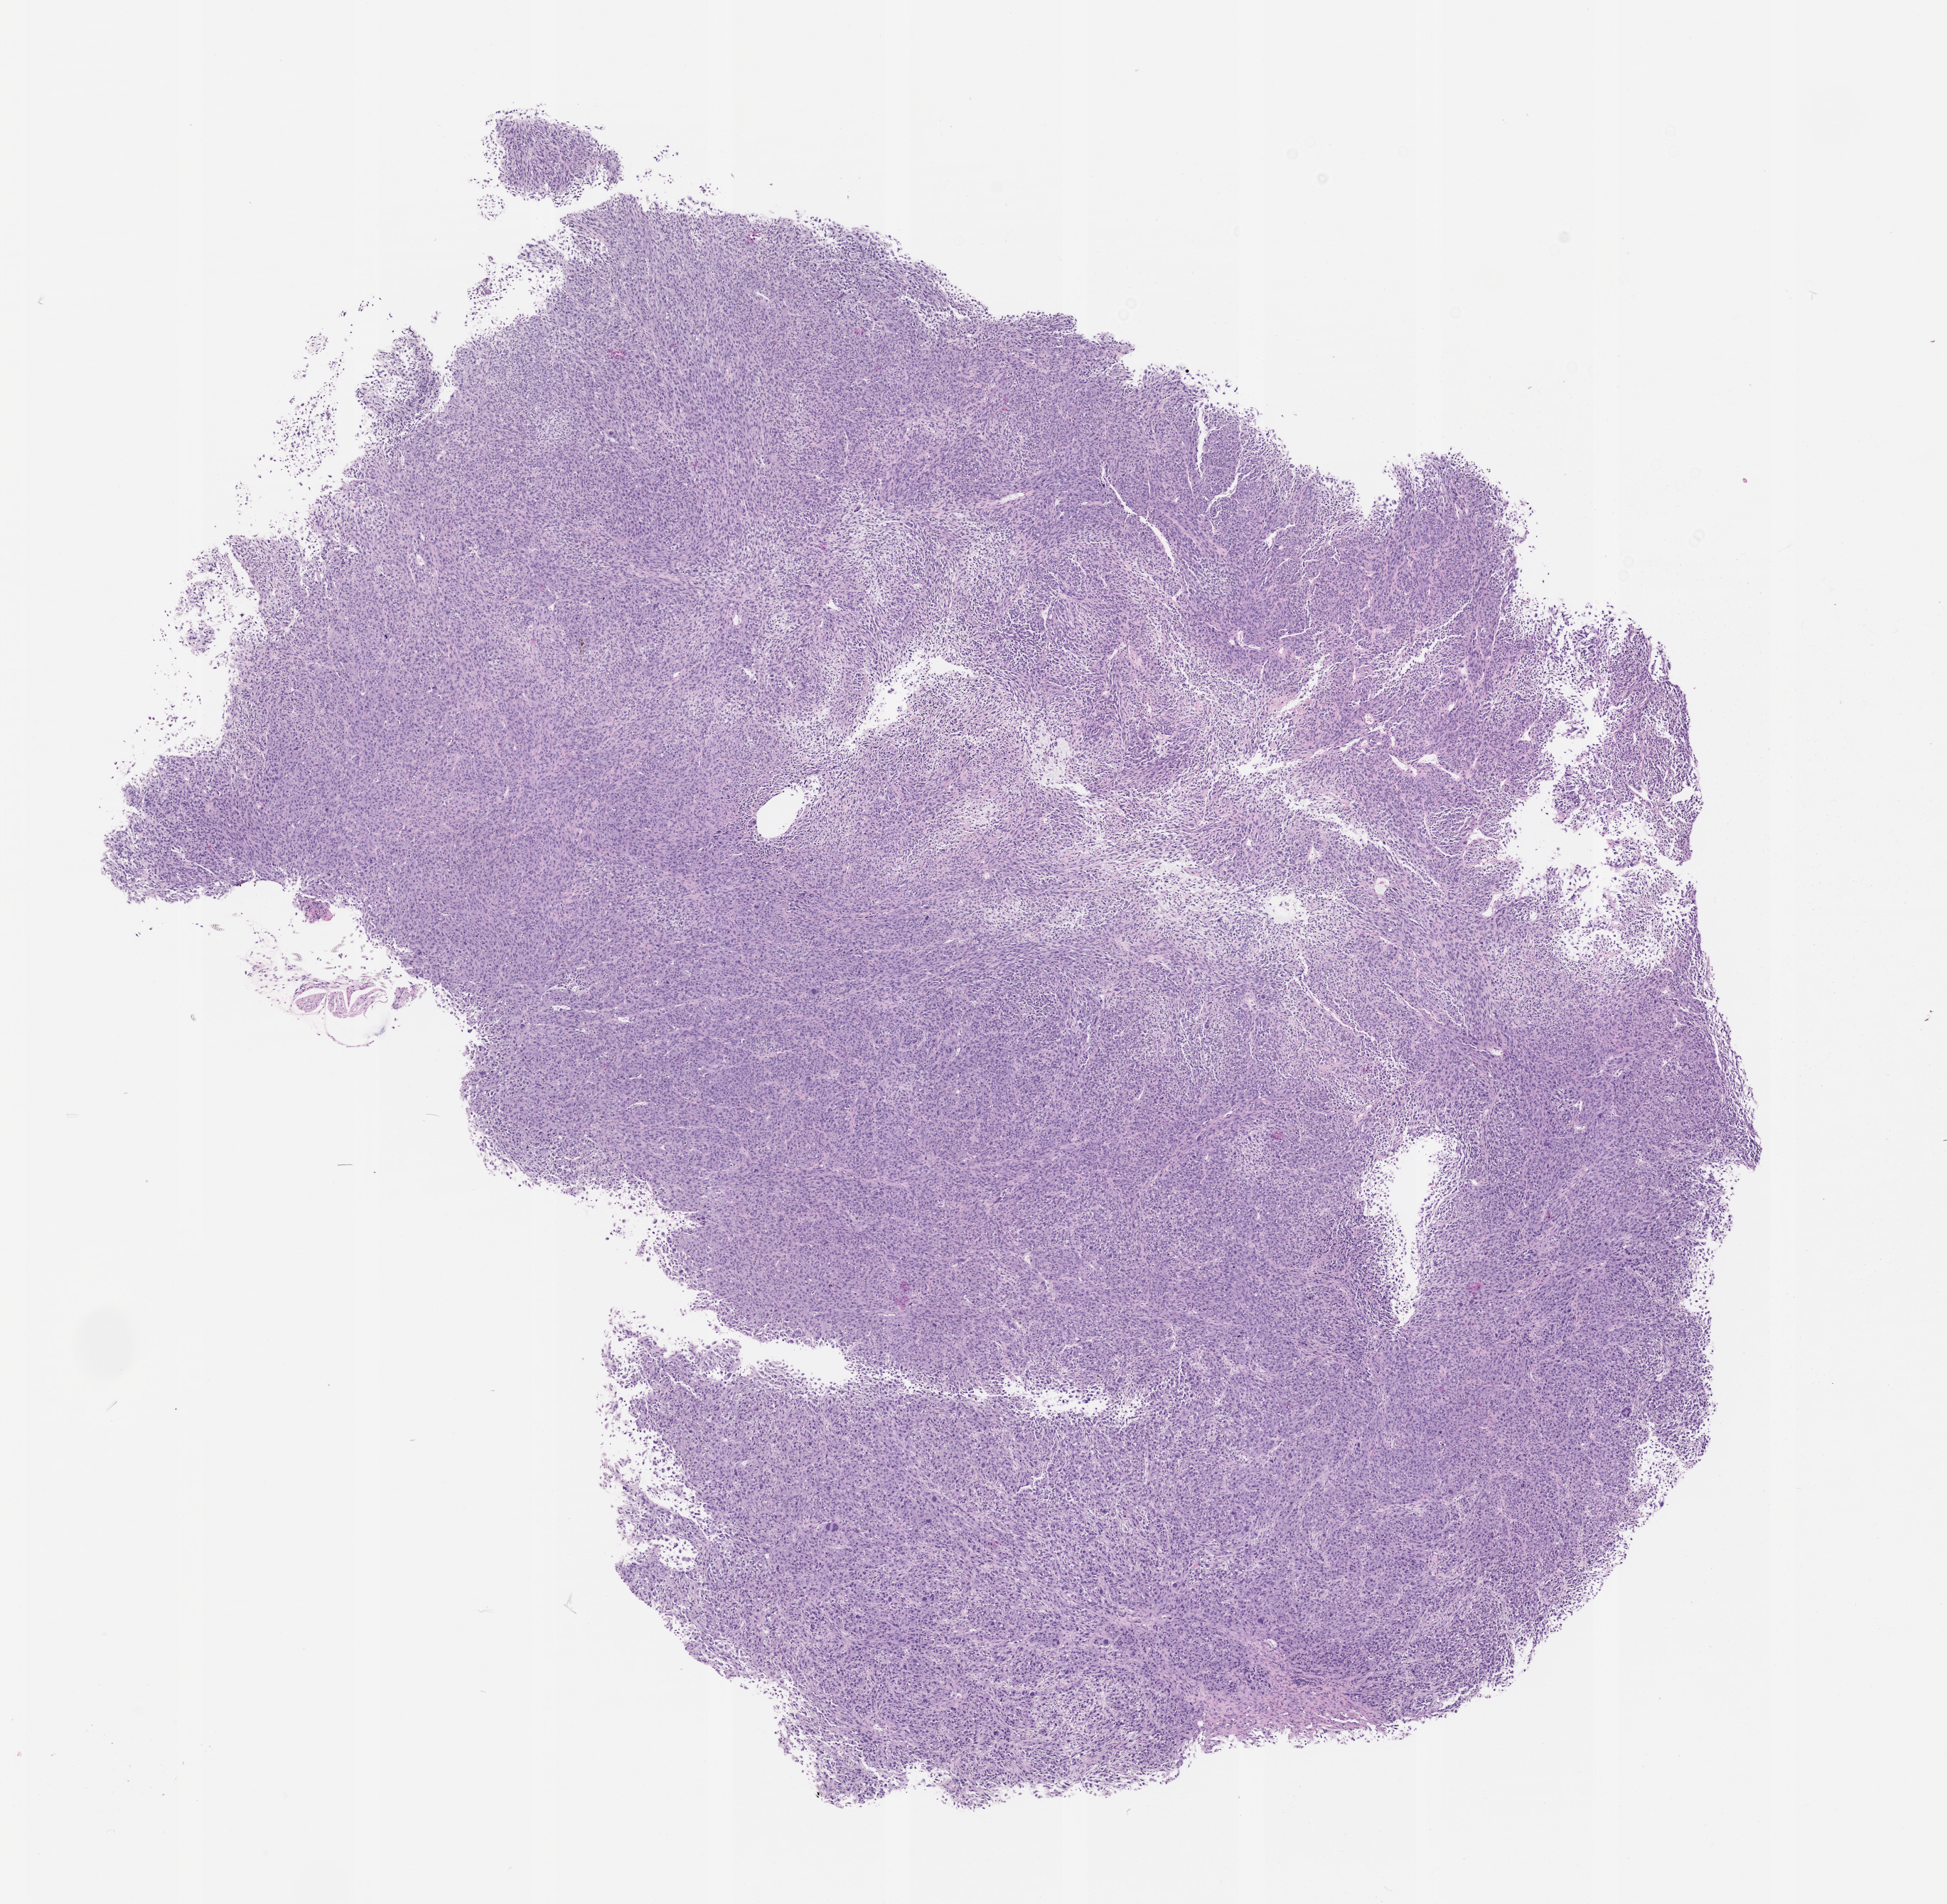
H&E whole-slide image of a patient-derived xenograft (PDX) tumor grown in a mouse, passage 0, shown as a low-resolution overview of the whole scanned area (about 11.0 x 10.8 mm); formalin-fixed paraffin-embedded section; originating tumor site category: bone.
Originating patient diagnosis: Osteosarcoma.